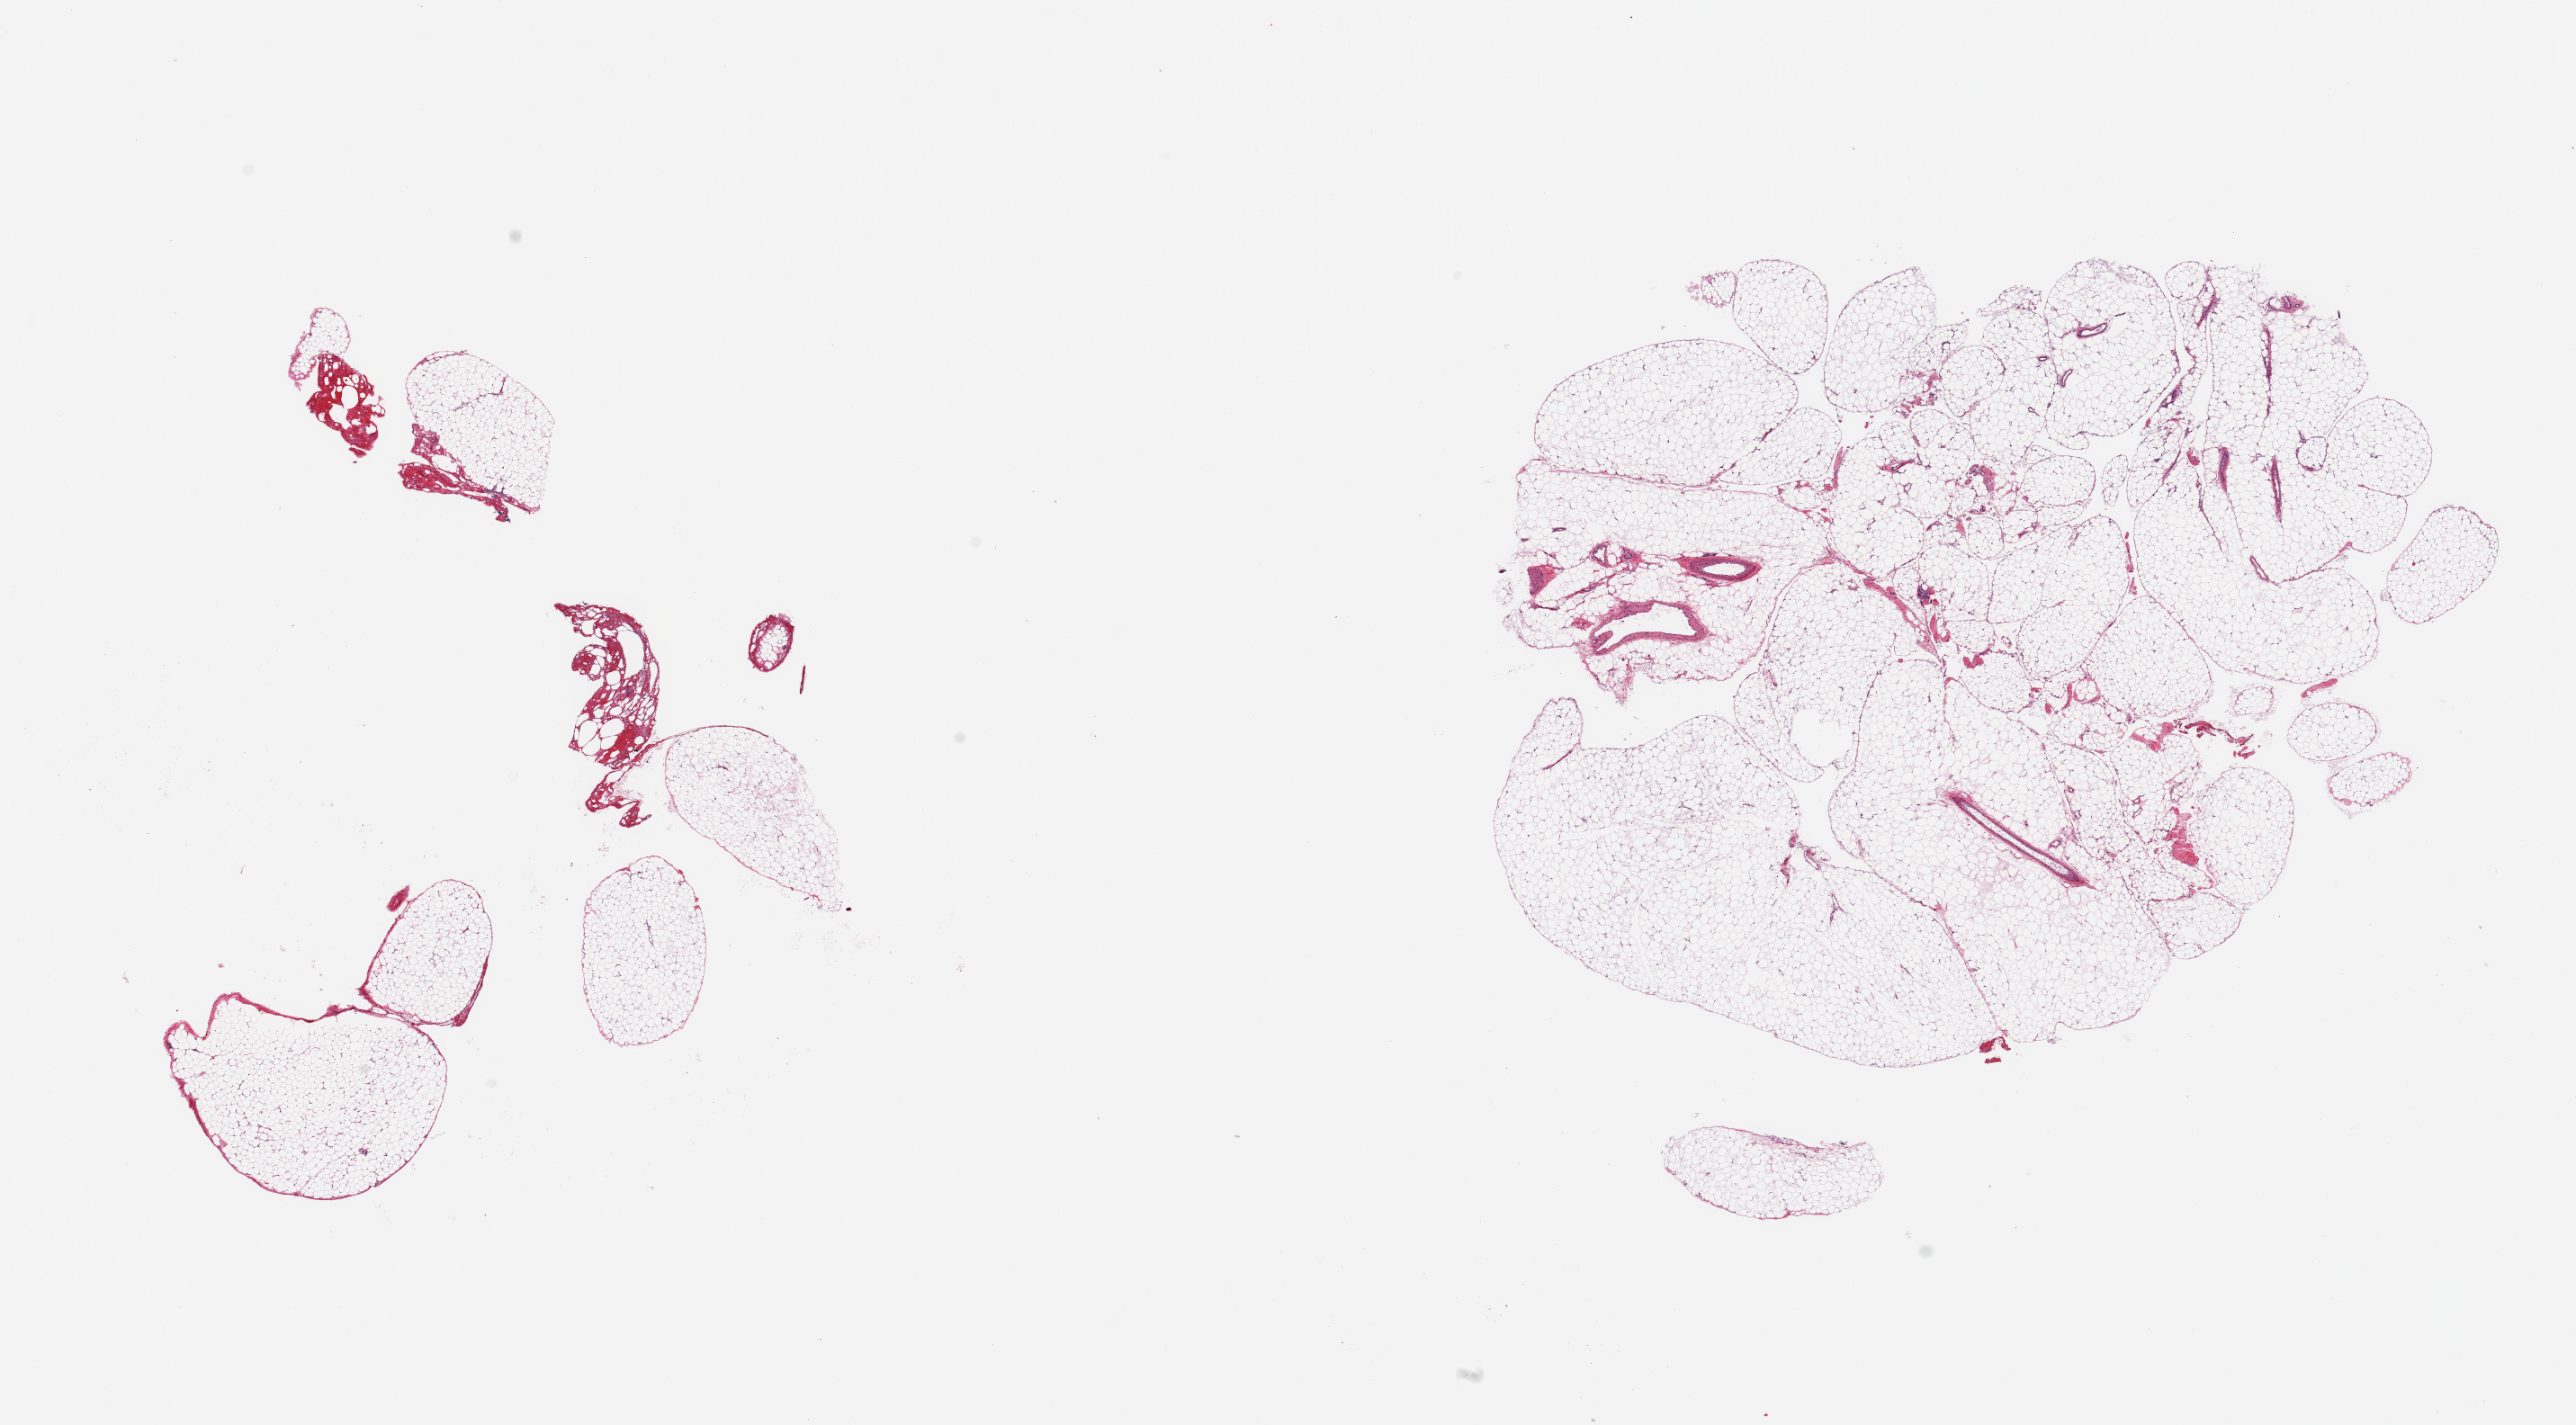
Digitized haematoxylin and eosin-stained section, a low-resolution overview of the entire scanned area, about 22.6 x 12.5 mm (slide scanned at 20x), PAXgene-fixed paraffin-embedded (PFPE) section, sampled site (target tissue): omentum, tissue donor sample. Donor: female.
Review note (as recorded): 2 pieces; 5% fibrovascular content.